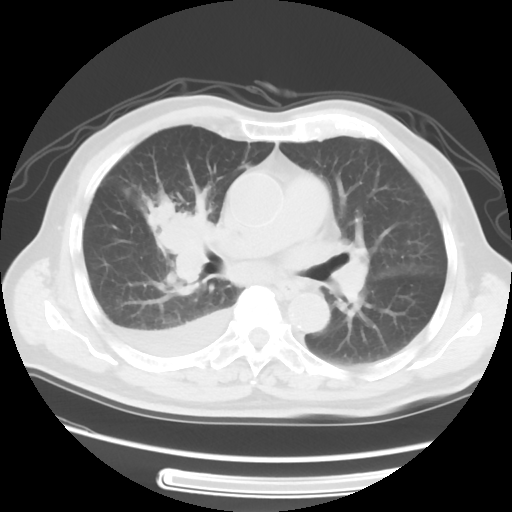
Chest CT, one axial slice; position 30 of 56 along the scan axis; lung window (W 1500 / L -600 HU); 5 mm slice thickness; 512 × 512 image matrix, field of view 360 × 360 mm. Patient: male, 77 years. Case-level facts recorded for this patient, not image findings: clinical TNM (as recorded): T3 N3 M1b; histopathological grade: G3.
Outlined on this slice (bounding box drawn by a radiologist):
- lung tumour (recorded histology: small cell carcinoma): bounding box <151,192,216,290> (left, top, right, bottom; pixels)